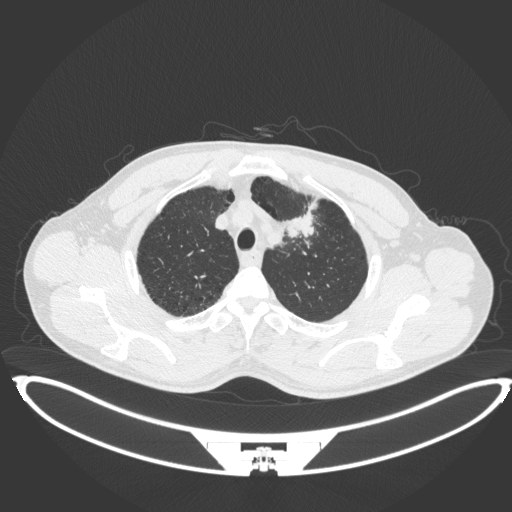
Chest CT, one axial slice; position 366 of 407 along the scan axis; lung window (W 1500 / L -600 HU); 1 mm slice thickness; 512 × 512 image matrix, field of view 457 × 457 mm. Male patient, age 60 years. From the clinical record (not read from this slice): clinical TNM (as recorded): T2a N0 M0; histopathological grade: G1-G2.
Annotated regions visible in this slice (rectangle marked by the reading radiologist):
- lung tumour (recorded histology: squamous cell carcinoma): bounding box (x1, y1, x2, y2) in pixels: (282, 210, 319, 240)